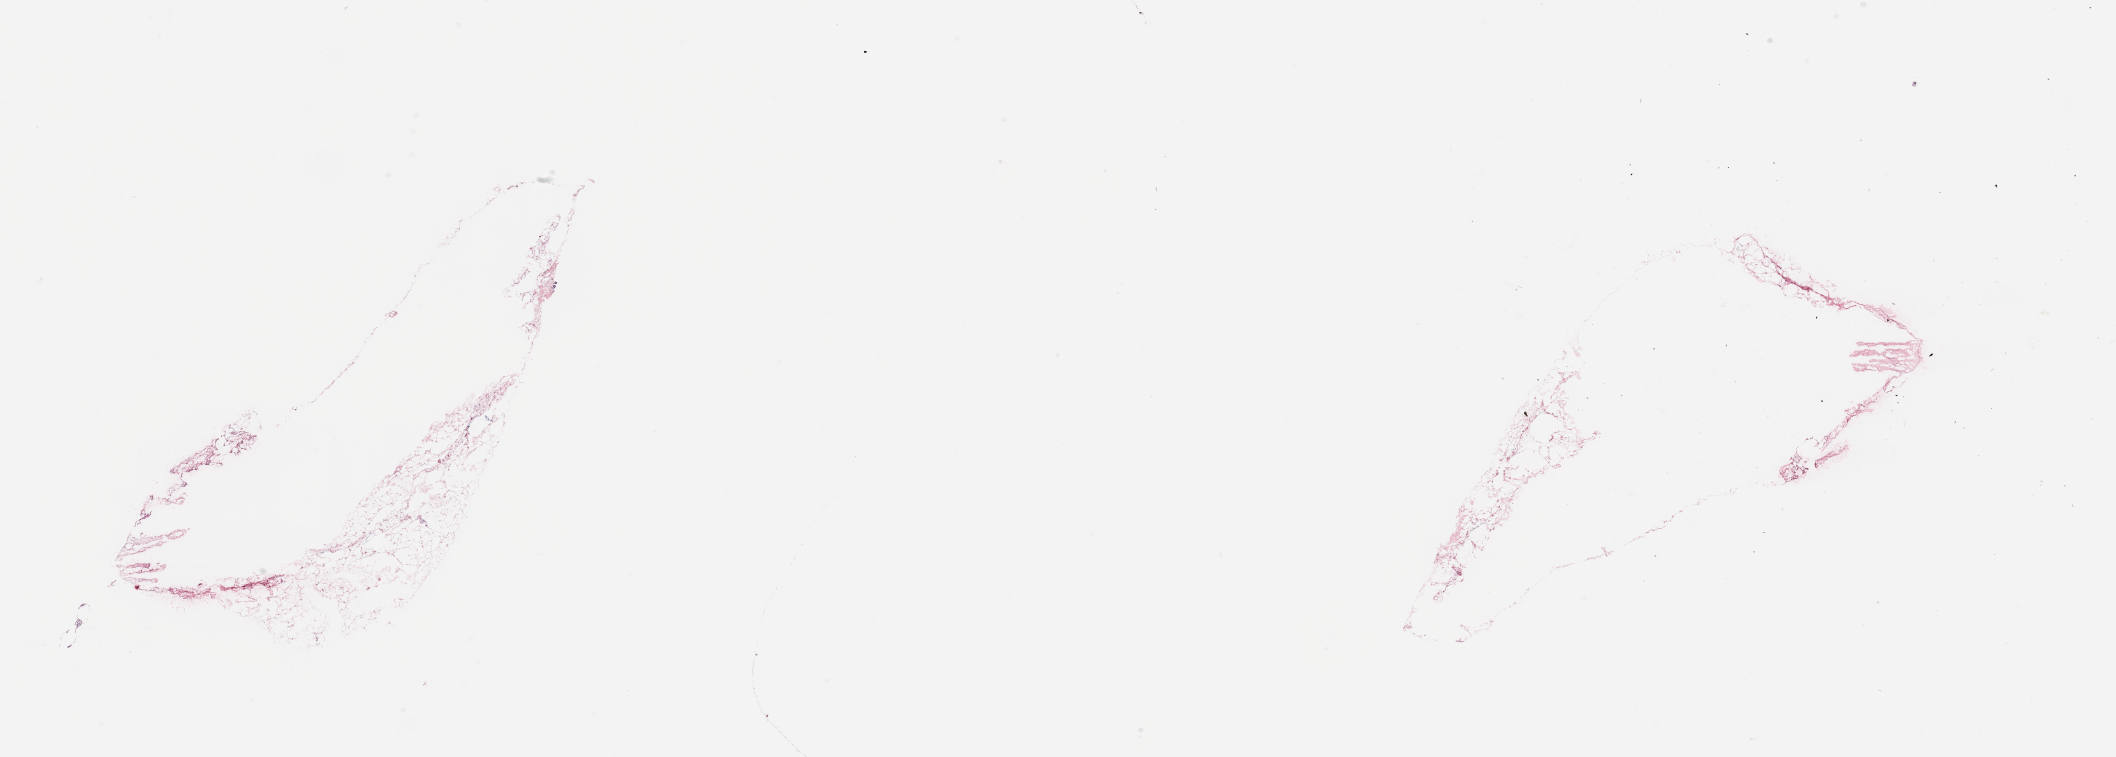
Digitized H&E tissue section (whole slide), a low-resolution overview of the entire scanned area, about 33.5 x 12.0 mm (slide scanned at 20x); tumour tissue sample, breast. Patient: female, age 40 years.
Diagnosis: Infiltrating duct carcinoma, NOS. AJCC pathologic stage: IIB.